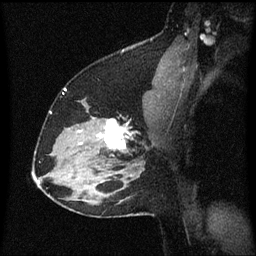
Breast MRI (dynamic contrast-enhanced), one sagittal slice. Position 43 of 60 along the scan axis. Dynamic contrast-enhanced series, image 2 of 3 at this slice position (ordered by acquisition). 1.5 T. TE 4.2 ms, TR 8.4 ms. 2 mm slice thickness. 256 × 256 image matrix. Patient: female, 37 years. Case-level facts recorded for this patient, not image findings: setting: breast cancer imaged before/during neoadjuvant chemotherapy; receptor status: HR-positive, HER2-negative.
Outlined on this slice (semi-automatic segmentation, software-assisted and operator-edited):
- analysis volume of interest (the breast-tissue region the enhancement analysis was run in; not a lesion): box from (x=94, y=118) to (x=138, y=157) px
- tumour enhancement mask (voxels above the 70 % enhancement threshold inside the analysis volume of interest): (x=102, y=120)–(x=130, y=151)